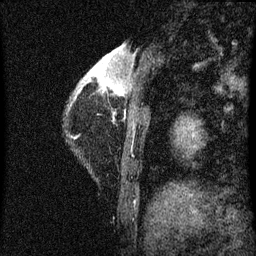
Breast MRI (dynamic contrast-enhanced), one sagittal slice; dynamic contrast-enhanced series, image 2 of 3 at this slice position (ordered by acquisition); 1.5 T; TE 4.2 ms, TR 8 ms; 256 × 256 image matrix, field of view 180 × 180 mm. Patient: female, 38 years.
Structures marked on this image (semi-automatically segmented with operator editing):
- analysis volume of interest (the breast-tissue region the enhancement analysis was run in; not a lesion): bounding box <71,44,136,125> (left, top, right, bottom; pixels)
- tumour enhancement mask (voxels above the 70 % enhancement threshold inside the analysis volume of interest): <115,88,122,95>